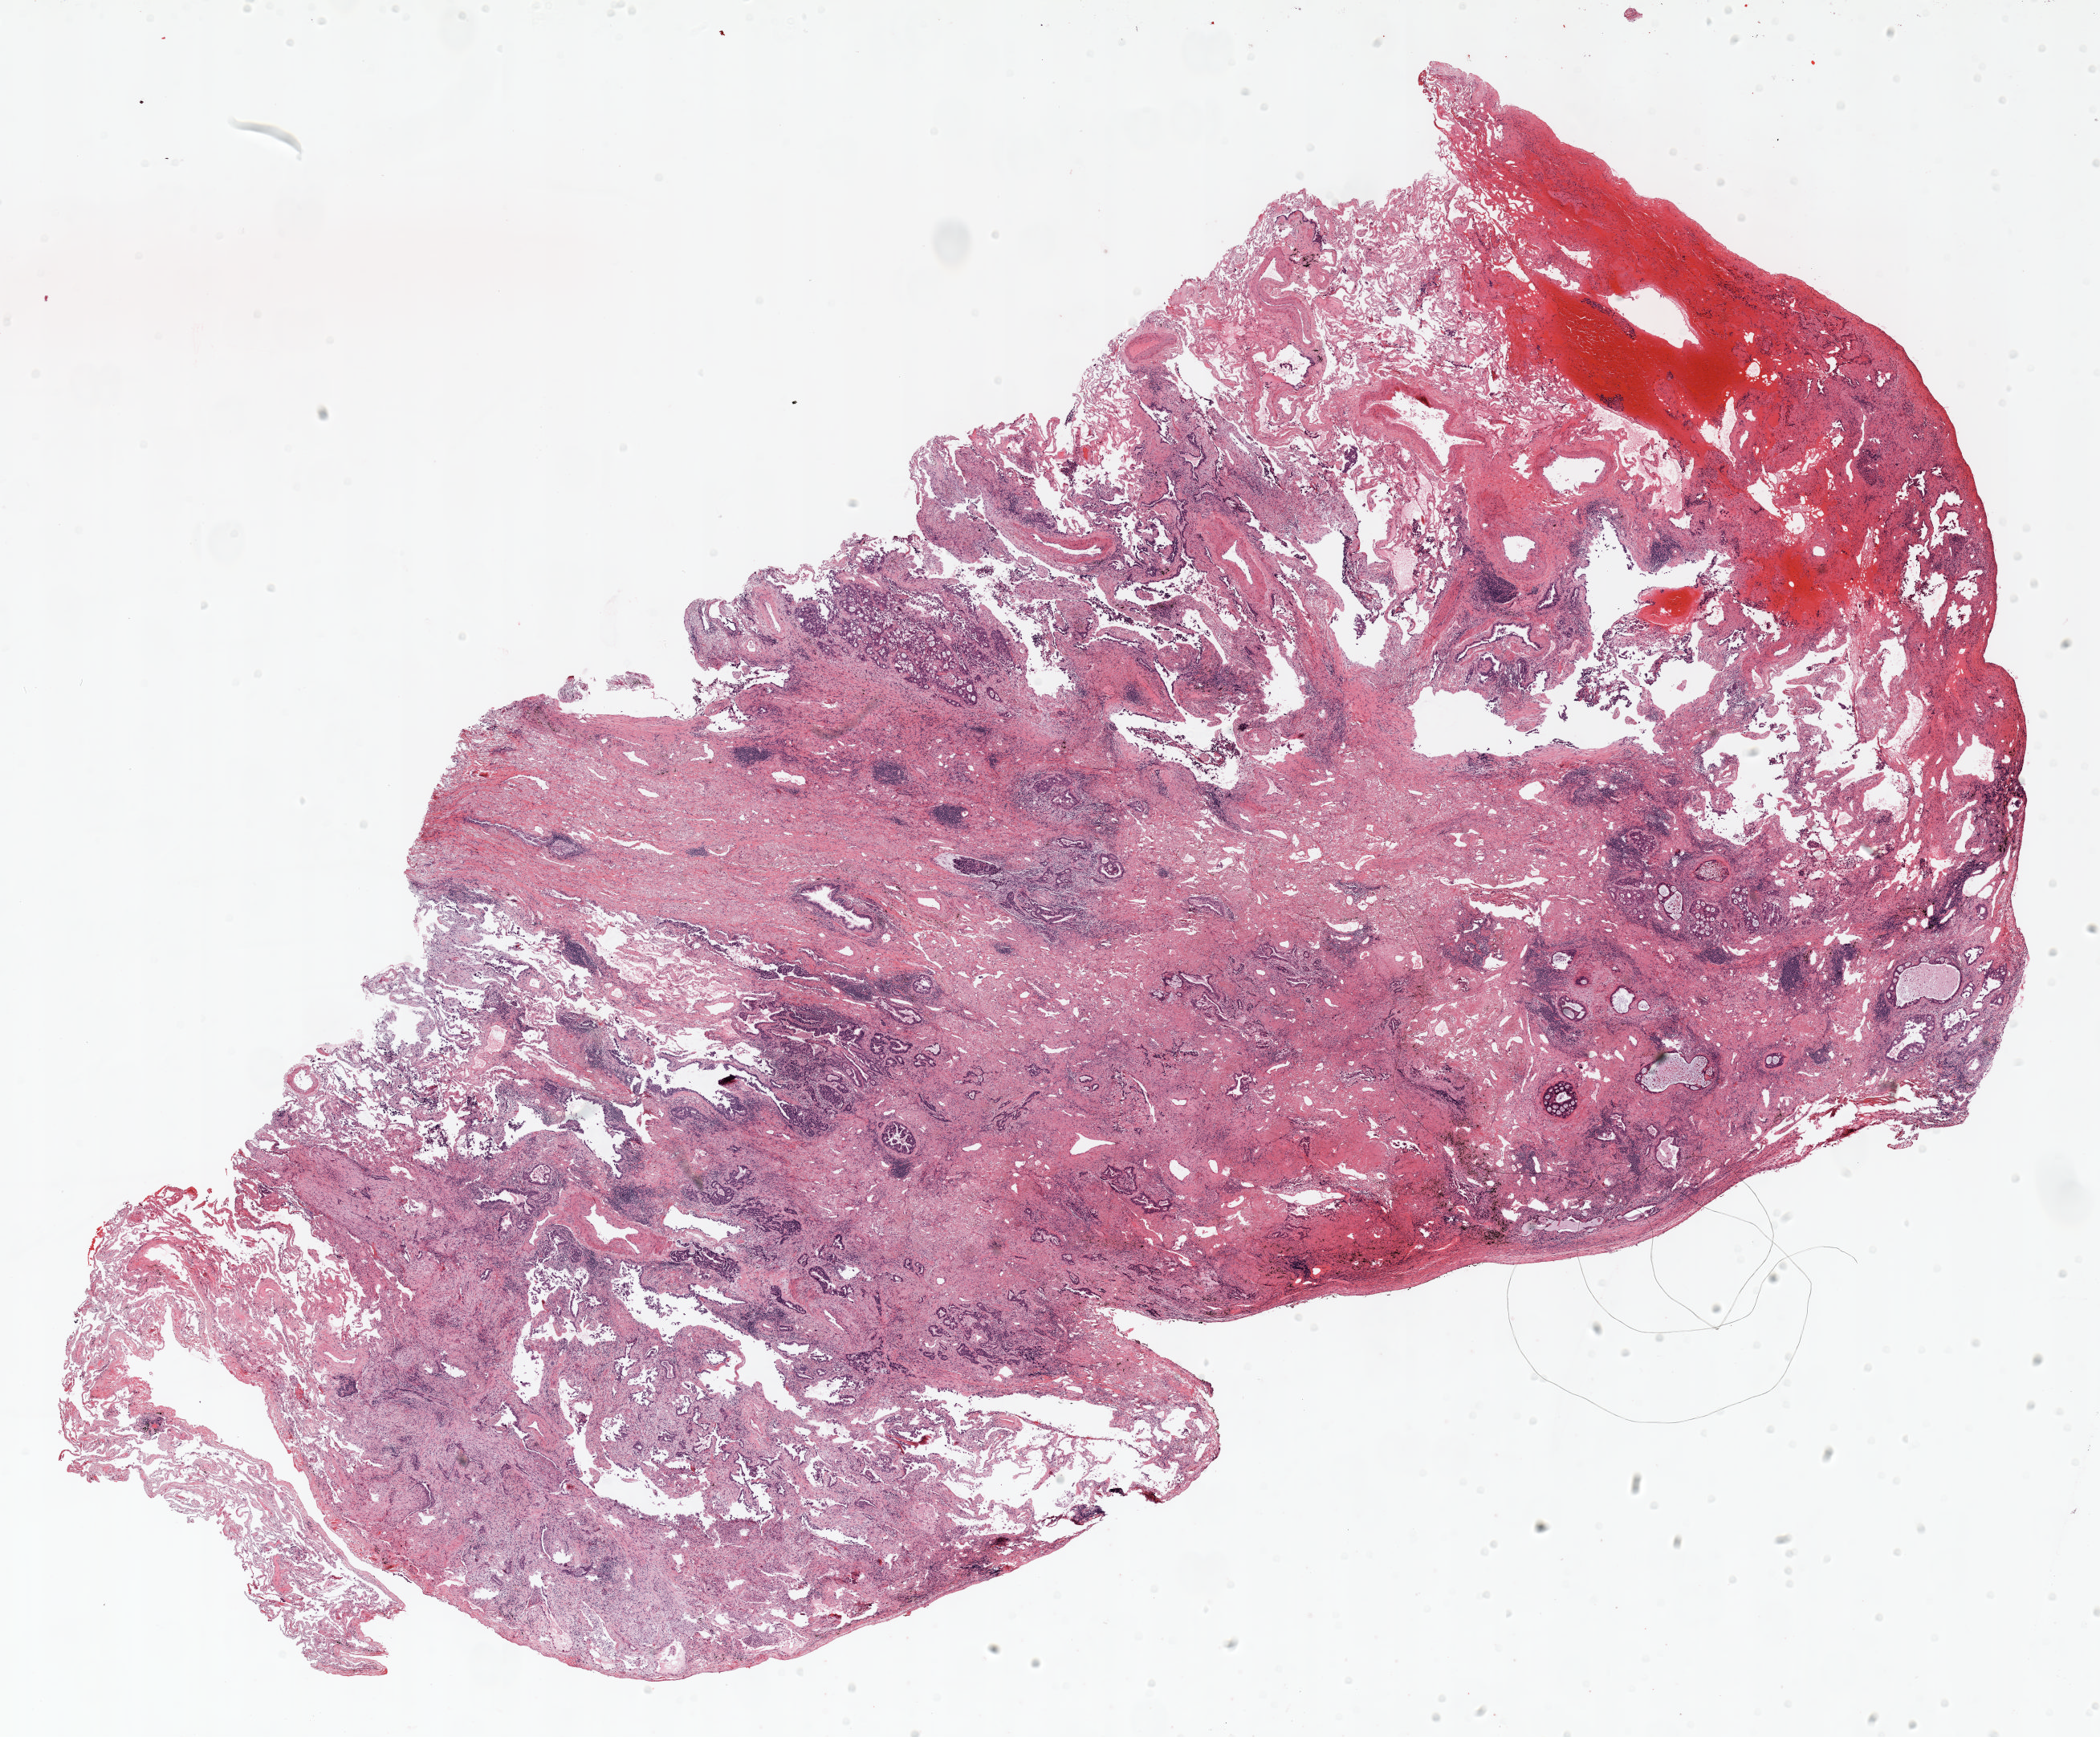
Whole-slide histology image, H&E-stained — a low-resolution overview of the entire scanned area, about 21.0 x 17.4 mm. Formalin-fixed paraffin-embedded (FFPE) section. Lung. Male patient, aged 73 at enrolment. Former smoker at enrolment. Grade: poorly differentiated (G3).
• ICD-O-3 topography: upper lobe of lung (C34.1)
• stage (AJCC 6th edition): IA
• primary tumour location (clinical record): right upper lobe
• participant's lung-cancer diagnosis: Adenocarcinoma, NOS (ICD-O-3 8140/3)
• tumour size (pathology): 30 mm